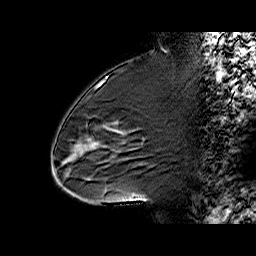
Breast MRI (dynamic contrast-enhanced), one sagittal slice. Position 32 of 60 along the scan axis. Dynamic contrast-enhanced series, time point 2 of 6 at this slice position (early post-contrast). 1.5 T. TE 6.3 ms, TR 32.4 ms. 4 mm slice thickness. 256 × 256 image matrix. Female patient. From the clinical record (not read from this slice): setting: breast cancer imaged before/during neoadjuvant chemotherapy; receptor status: triple-negative.
Outlined on this slice (semi-automatically segmented with operator editing):
- analysis volume of interest (the breast-tissue region the enhancement analysis was run in; not a lesion): bounding box [x1, y1, x2, y2] px = [65, 88, 139, 187]
- tumour enhancement mask (voxels above the 100 % enhancement threshold inside the analysis volume of interest): [91, 143, 94, 146]